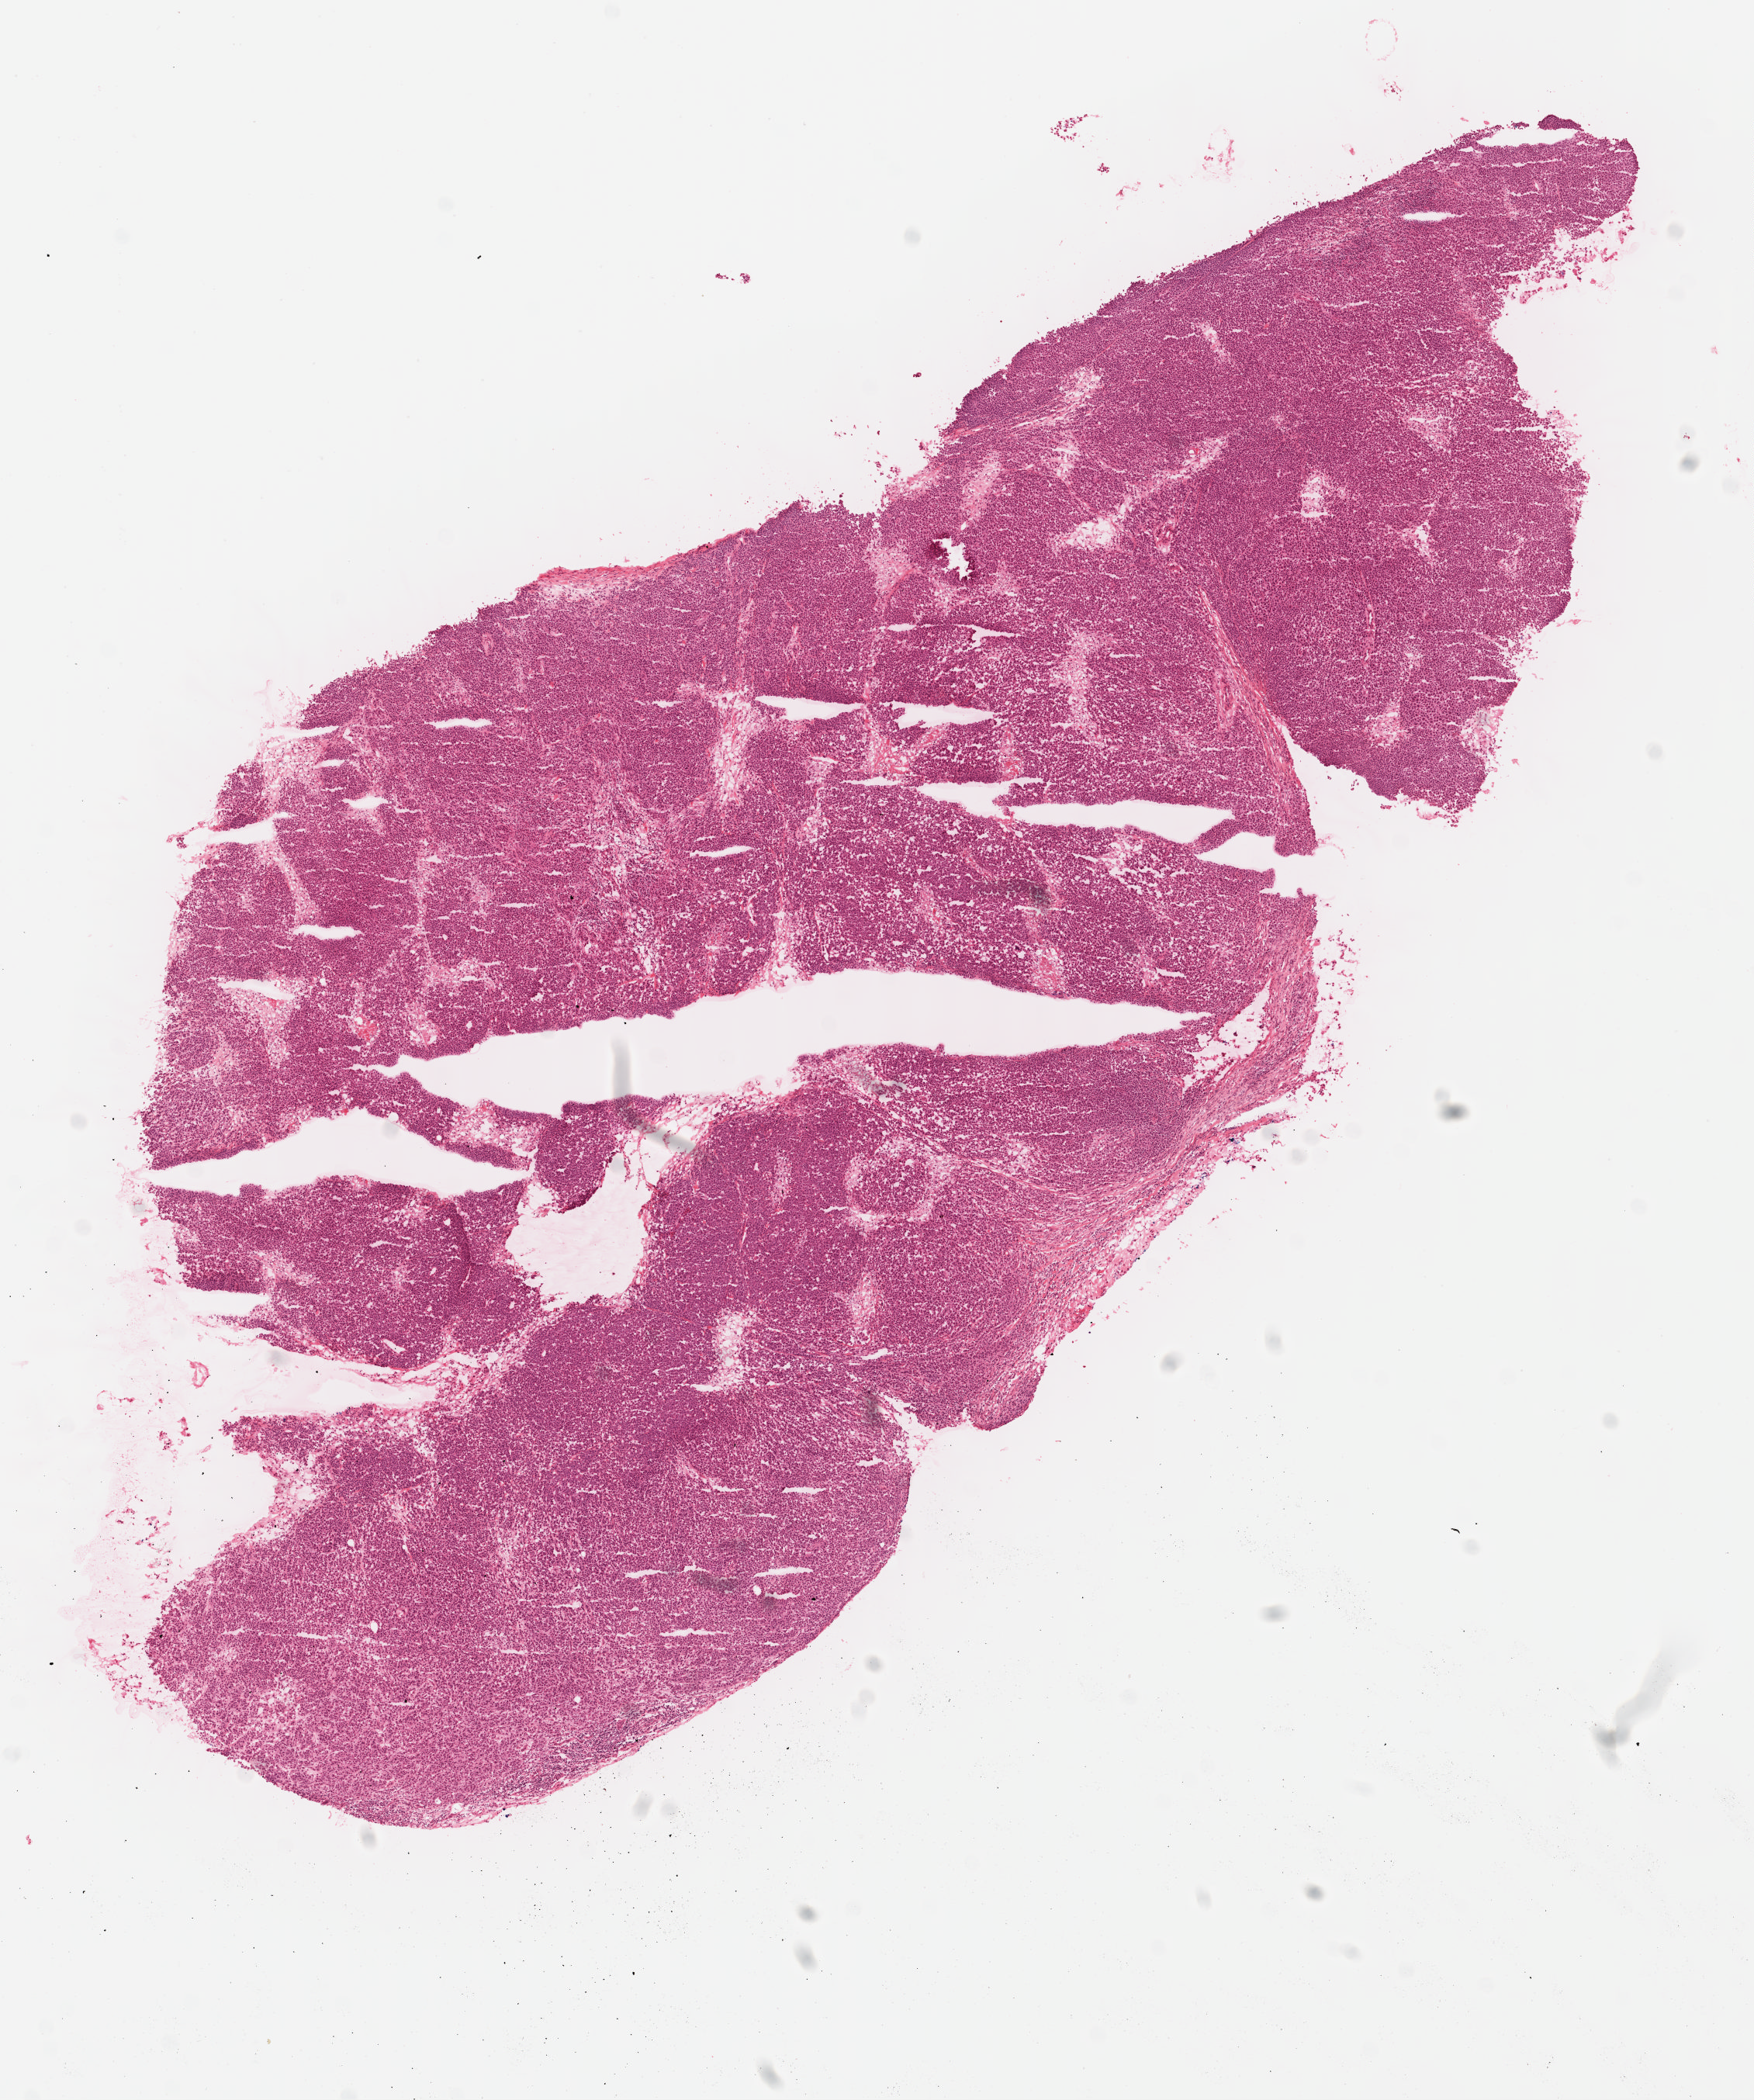
Digitized H&E tissue section (whole slide), whole scanned area (about 8.9 x 10.6 mm, slide scanned at 40x) shown as a low-resolution overview. FFPE section. Skin, primary tumour sample. Patient: male, age at initial diagnosis 72 years.
Pathologic diagnosis: Malignant melanoma, NOS.